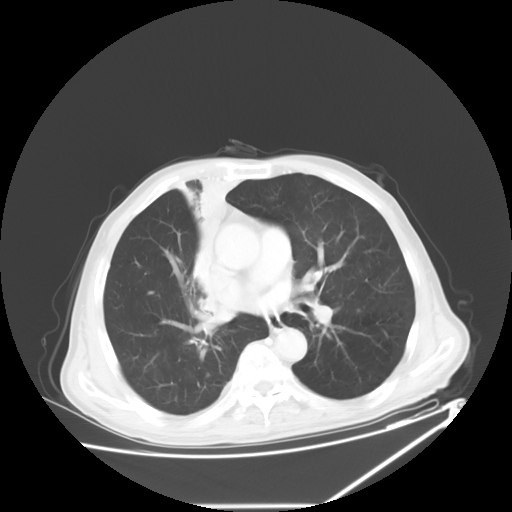
Chest CT, one axial slice; 120 kVp; lung window (W 1500 / L -600 HU); 512 × 512 image matrix, field of view 410 × 410 mm. Patient: male, 73 years. From the clinical record (not read from this slice): clinical TNM (as recorded): T2a N1 M0.
Structures marked on this image (bounding box drawn by a radiologist):
- lung tumour (recorded histology: squamous cell carcinoma): bounding box [x1, y1, x2, y2] px = [184, 171, 234, 327]